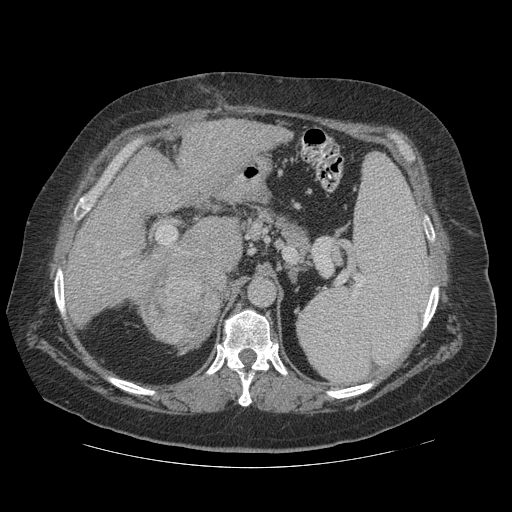
Contrast-enhanced abdominal CT (liver protocol), one axial slice. Slice 73 of 121 in the series (ordered by position). Reconstruction kernel STANDARD. Soft-tissue window (W 400 / L 40 HU). 2.5 mm slice thickness. 512 × 512 image matrix, field of view 420 × 420 mm. From the clinical record (not read from this slice): diagnosis: hepatocellular carcinoma (patient treated with transarterial chemoembolisation; whether this scan precedes or follows treatment is not stated here); TNM stage (as recorded): Stage-IIIA.
Annotated regions visible in this slice (semi-automatic segmentation, software-assisted and operator-edited):
- liver parenchyma outside the tumour (the mass and vessels are separate outlines, so this box may not span the whole liver): bounding box <66,118,292,312> (left, top, right, bottom; pixels)
- mass: <137,256,219,349>
- liver vessels: <83,135,212,290>